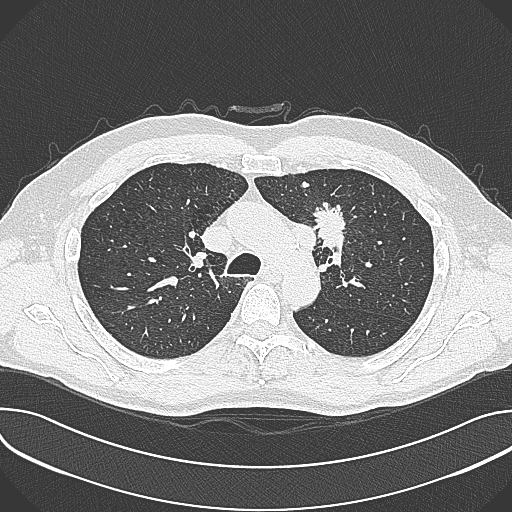
Axial slice from a low-dose chest CT screening exam, baseline screening round, lung window (W 1500 / L -600 HU), 1 mm slice thickness, lung (sharp) reconstruction kernel (B80f), 120 kVp, 512 × 512 image matrix. Male participant, aged 59 years at enrolment. Current smoker at enrolment.
- Expert-annotated lung lesion, box from (x=302, y=197) to (x=361, y=257) px.
- The screening reader recorded 2 non-calcified nodules or masses ≥4 mm on this exam (left upper lobe, left upper lobe); which of them this box marks is not recorded.